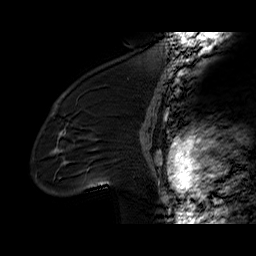
Breast MRI (dynamic contrast-enhanced), one sagittal slice. Position 42 of 60 along the scan axis. Dynamic contrast-enhanced series, time point 2 of 6 at this slice position (early post-contrast). 1.5 T. TE 6.2 ms, TR 32.4 ms. 4 mm slice thickness. 256 × 256 image matrix, field of view 200 × 200 mm. Female patient. From the clinical record (not read from this slice): setting: breast cancer imaged before/during neoadjuvant chemotherapy; receptor status: triple-negative.
Annotated regions visible in this slice (semi-automatically segmented with operator editing):
- analysis volume of interest (the breast-tissue region the enhancement analysis was run in; not a lesion): bounding box <36,97,134,196> (left, top, right, bottom; pixels)
- tumour enhancement mask (voxels above the 100 % enhancement threshold inside the analysis volume of interest): <55,106,65,138>